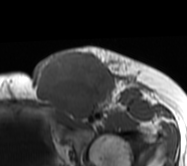
MRI of an extremity soft-tissue mass, one axial slice; position 38 of 62 along the scan axis; MR volume resampled by the dataset authors to the PET/CT grid (not the native acquisition matrix); 3.27 mm slice thickness; 187 × 166 image matrix, field of view 183 × 162 mm. Female patient. Case-level facts recorded for this patient, not image findings: histological type: leiomyosarcoma; grade: high; site of the primary tumour: groin.
Structures marked on this image (expert contour drawn on MRI and transferred to this co-registered scan by the dataset authors):
- gross tumour volume including surrounding oedema: box from (x=32, y=46) to (x=149, y=123) px
- gross tumour volume (mass): (x=34, y=49)–(x=115, y=120)